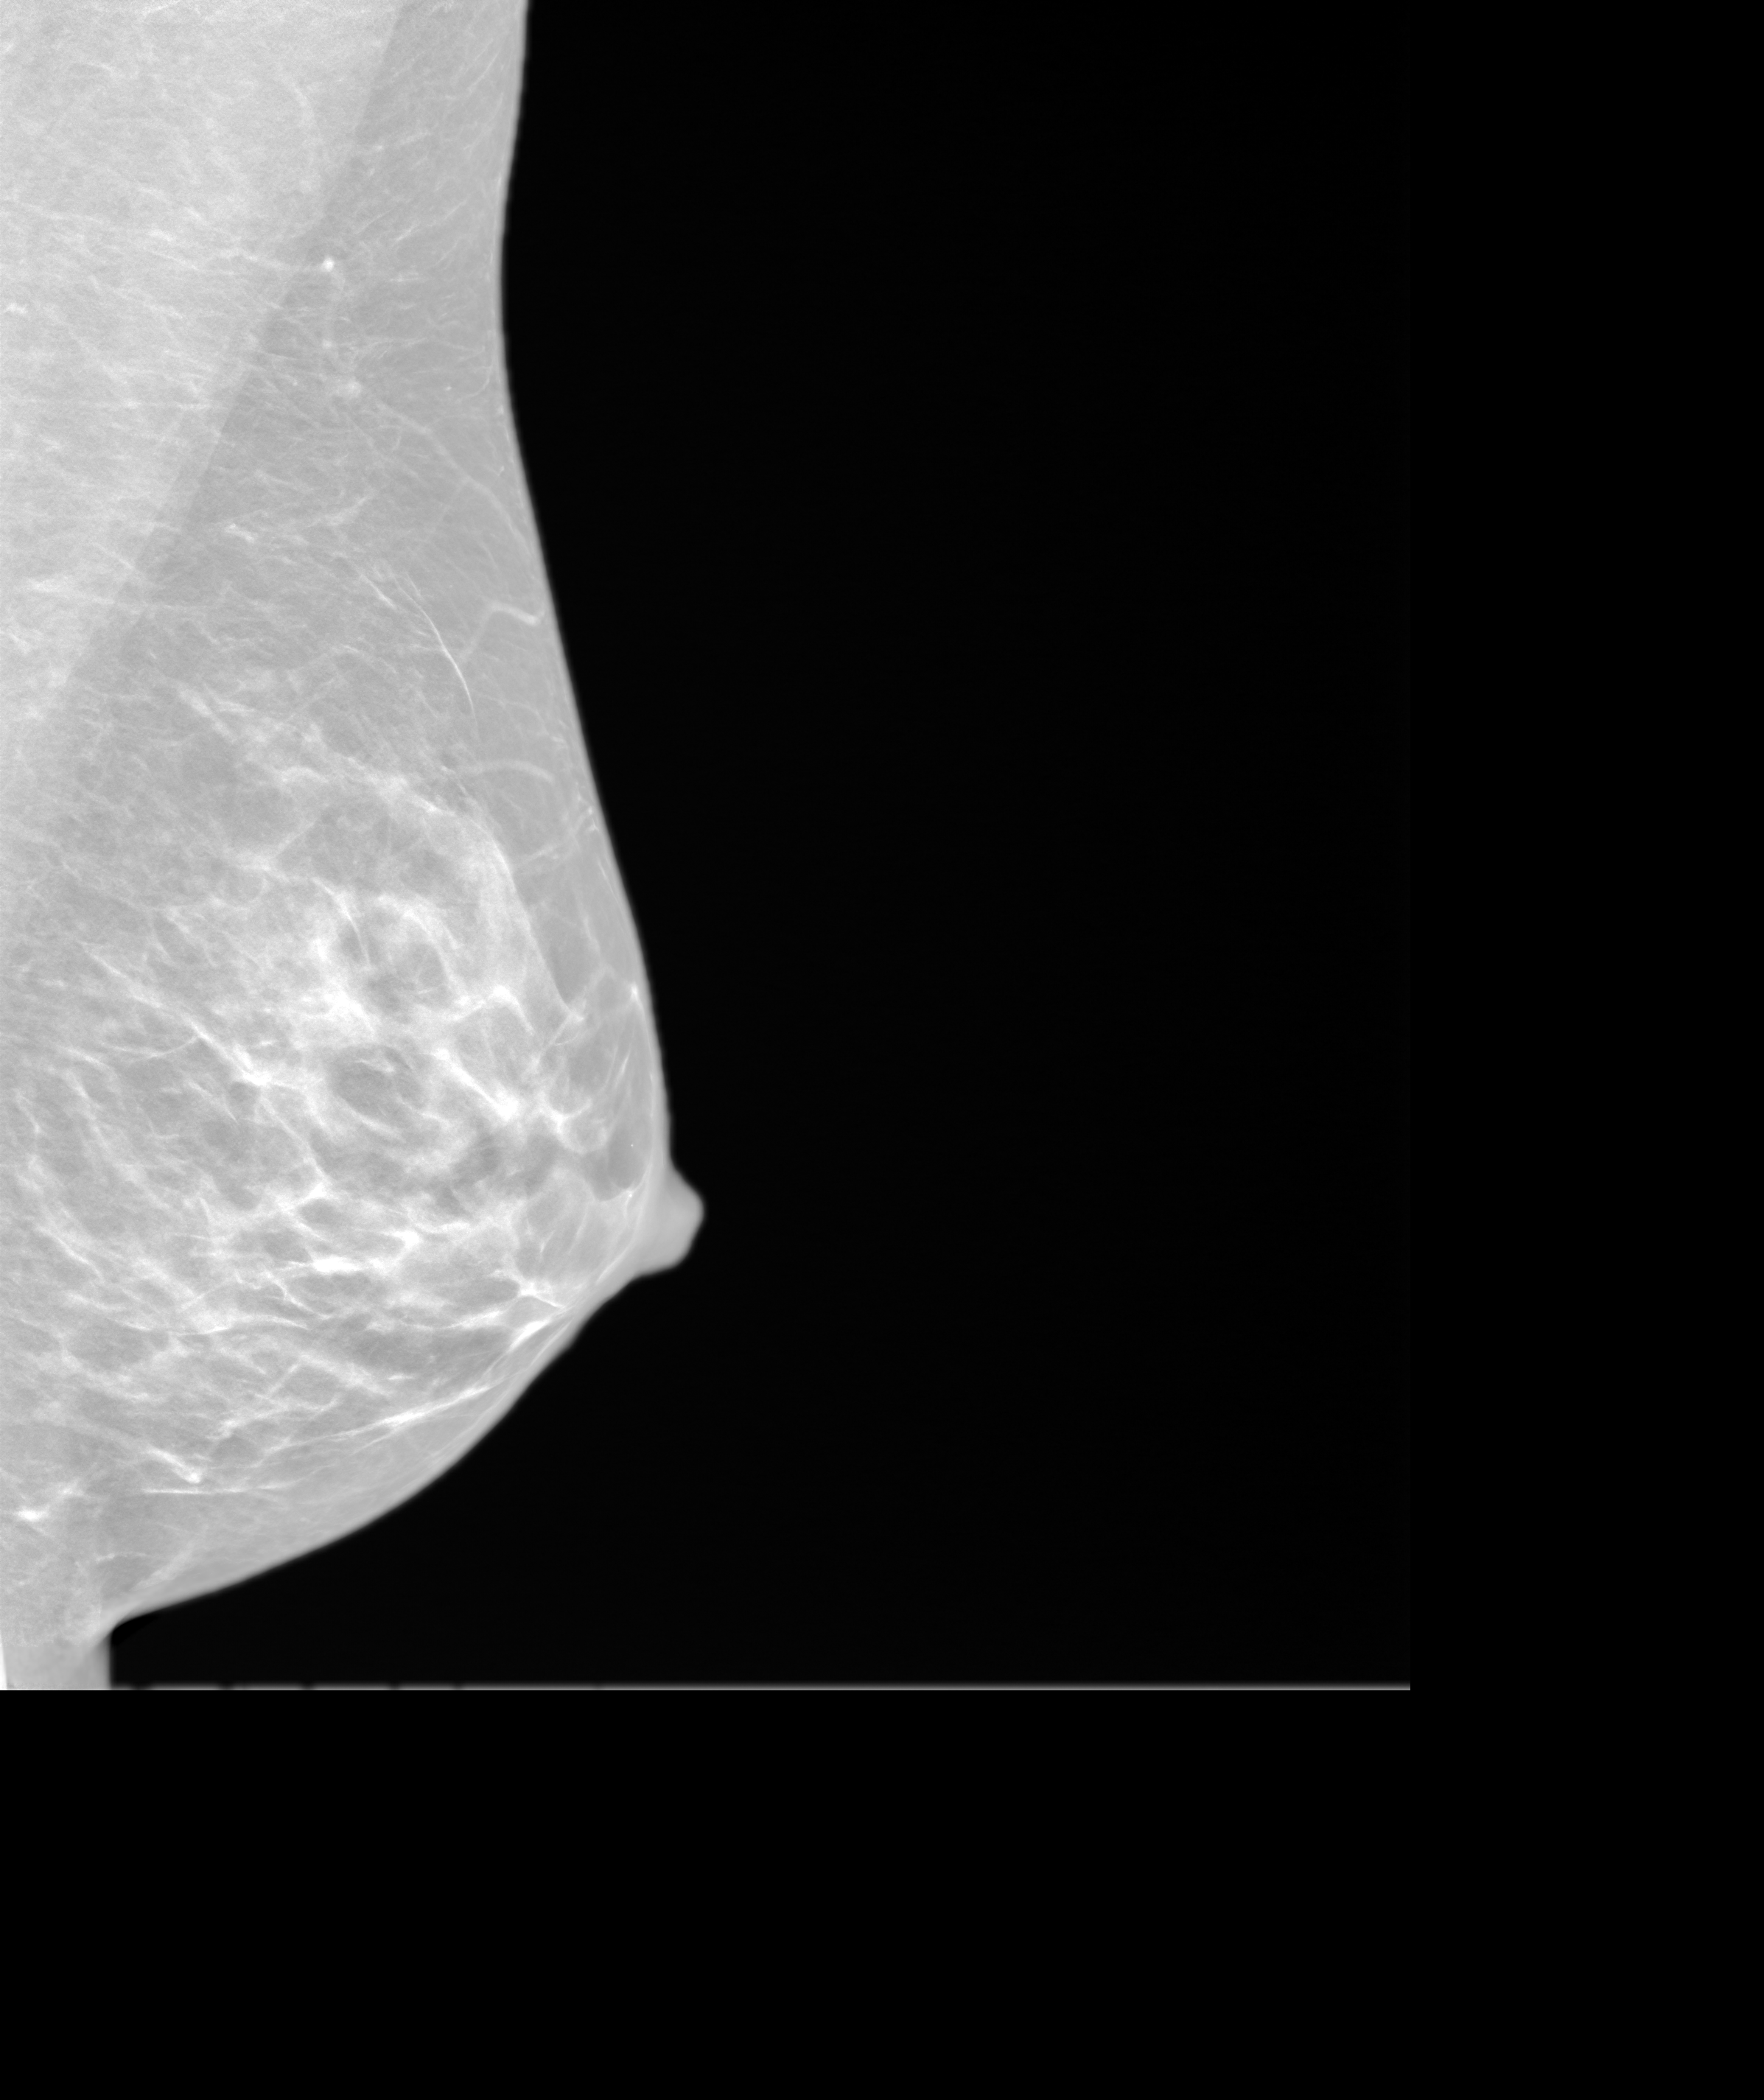
Screening examination. Female patient, age 44 years.
Image type: synthesized 2-D view from tomosynthesis. Breast: left. Projection: medio-lateral oblique projection.